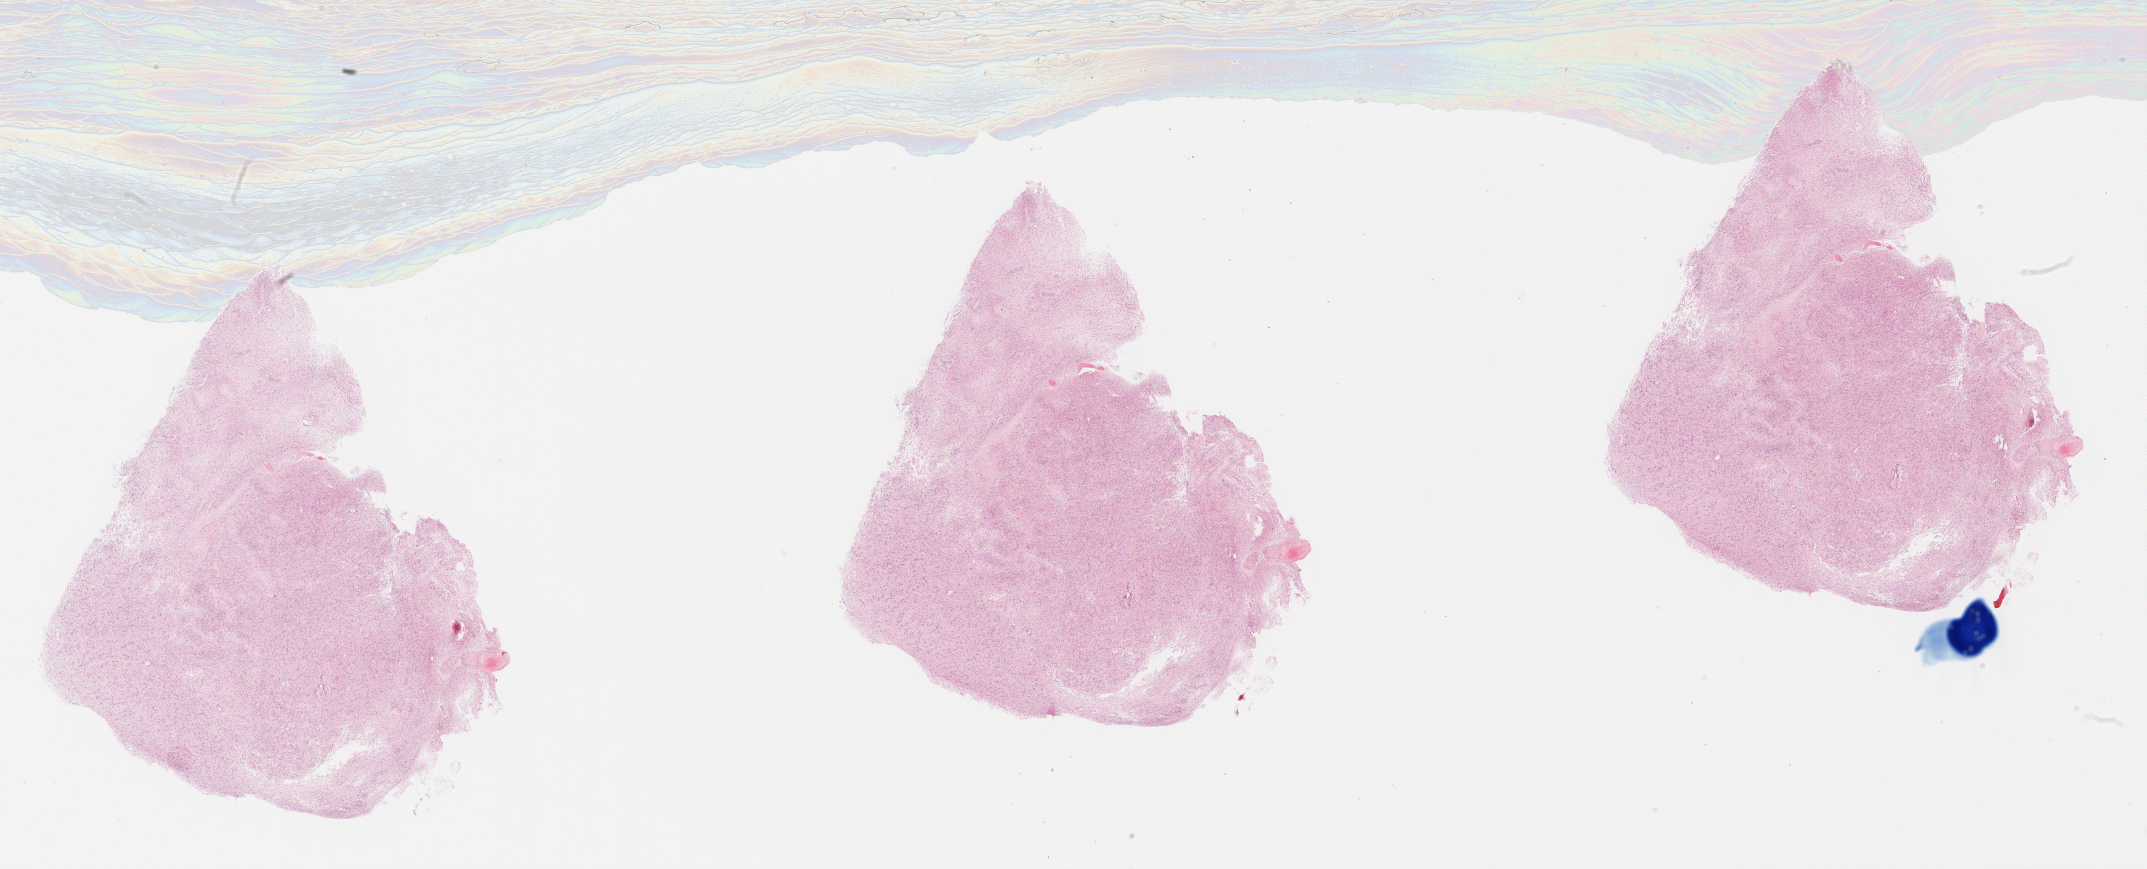
Whole-slide histology image, H&E — low-resolution overview of the scanned area, about 34.7 x 14.0 mm; formalin-fixed paraffin-embedded (FFPE) diagnostic section; brain, primary tumour sample. Patient: male, age at initial diagnosis 76 years.
Diagnosis: Glioblastoma.